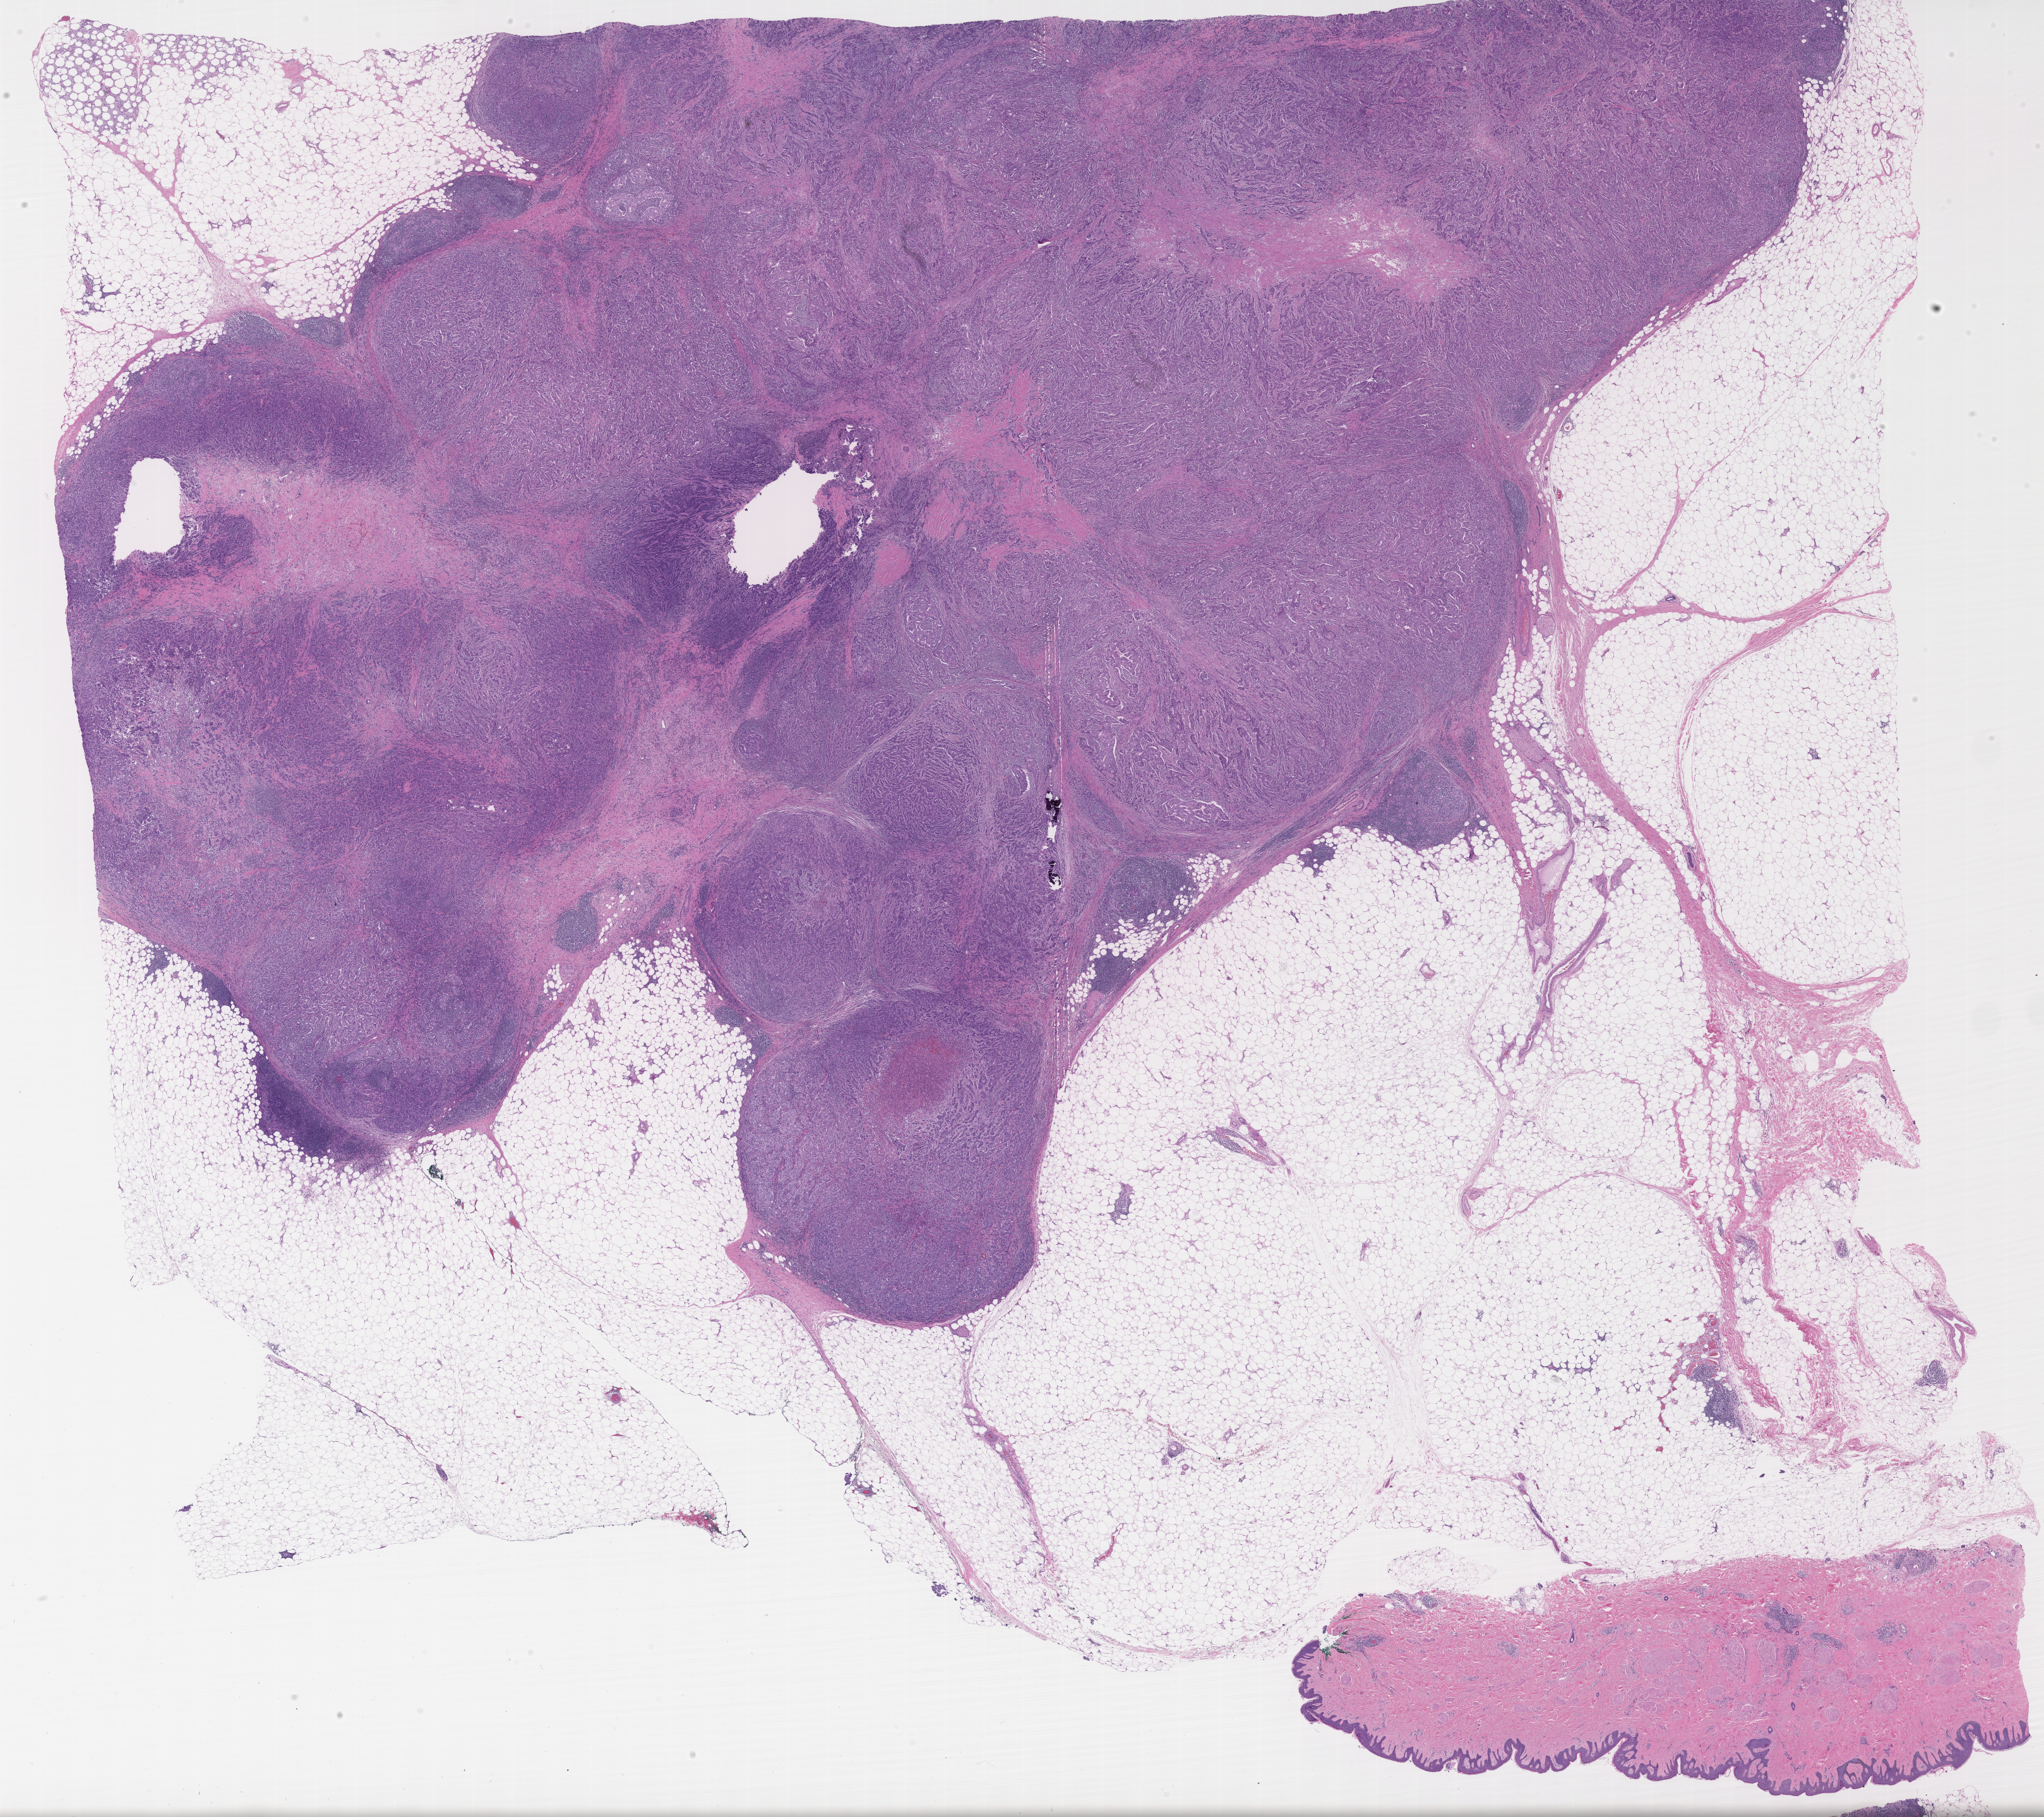
Whole-slide image, haematoxylin and eosin stain, shown as a low-resolution overview of the whole scanned area (about 26.1 x 23.2 mm). Formalin-fixed, paraffin-embedded (FFPE) tissue. Specimen: primary tumor. Anatomic site: breast (left). Male patient; age at initial diagnosis 79 years. Composition of this section per pathologist review: tumor cells 80%, tumor nuclei 80%, stromal cells 17%, necrosis 3%, normal cells 0%. Infiltration values recorded for this section: lymphocyte infiltration 9%, monocyte infiltration 2%, neutrophil infiltration 4%.
* diagnosis: Infiltrating duct carcinoma, NOS
* section: top of the tissue portion